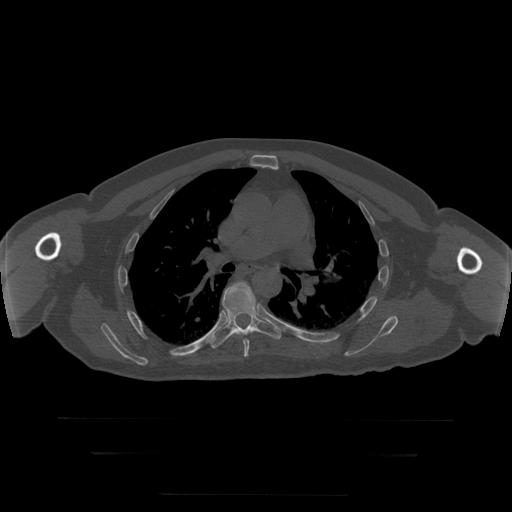
CT including the spine, one axial slice; position 194 of 397 along the scan axis; reconstruction kernel STANDARD; 120 kVp; bone window (W 1800 / L 400 HU); 1.25 mm slice thickness; 512 × 512 image matrix, field of view 510 × 510 mm. Patient age 73 years. Case-level facts recorded for this patient, not image findings: primary cancer: prostate.
Annotated regions visible in this slice (semi-automatic segmentation, software-assisted and operator-edited):
- T6 vertebra: bounding box (x1, y1, x2, y2) in pixels: (224, 297, 249, 357)
- T7 vertebra: (210, 282, 281, 349)